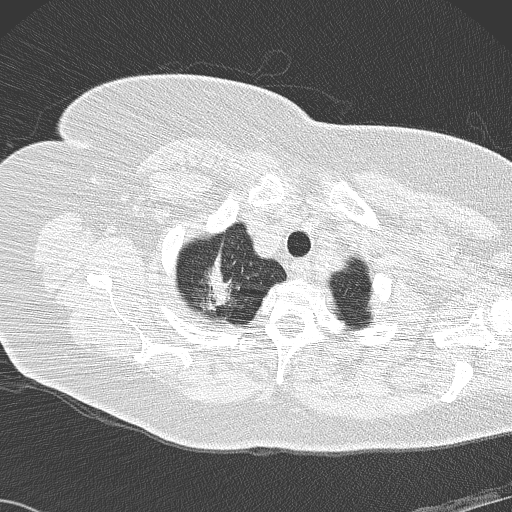
Low-dose screening chest CT, axial slice. Second annual screen. Lung window (W 1500 / L -600 HU). Slice 16 of 146 in the series. Female, age 72 years at enrolment. Former smoker at enrolment.
Expert reader's lesion annotation, bounding box [x1, y1, x2, y2] px = [183, 246, 257, 326]. The screening reader recorded 4 non-calcified nodules or masses ≥4 mm on this exam (right lower lobe, right lower lobe, right lower lobe, right upper lobe); which of them this box marks is not recorded. Official screen result: positive, other. Lung cancer was diagnosed 52 days after this screen: bronchiolo-alveolar adenocarcinoma, NOS, right upper lobe, stage IIIB (AJCC 6th edition), 45 mm at pathology.